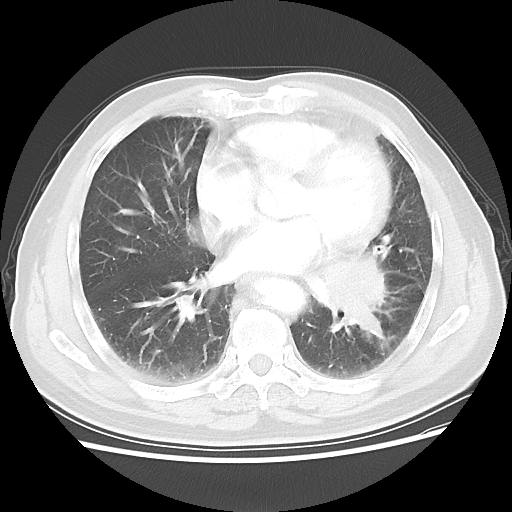
Chest CT, one axial slice; slice 26 of 56 in the series (ordered by position); reconstruction kernel LUNG; lung window (W 1500 / L -600 HU); 5 mm slice thickness; 512 × 512 image matrix, field of view 360 × 360 mm. Male patient, age 75 years. Case-level facts recorded for this patient, not image findings: clinical TNM (as recorded): T3 N0 M0.
Outlined on this slice (rectangle marked by the reading radiologist):
- lung tumour (recorded histology: squamous cell carcinoma): bounding box (x1, y1, x2, y2) in pixels: (304, 248, 397, 347)